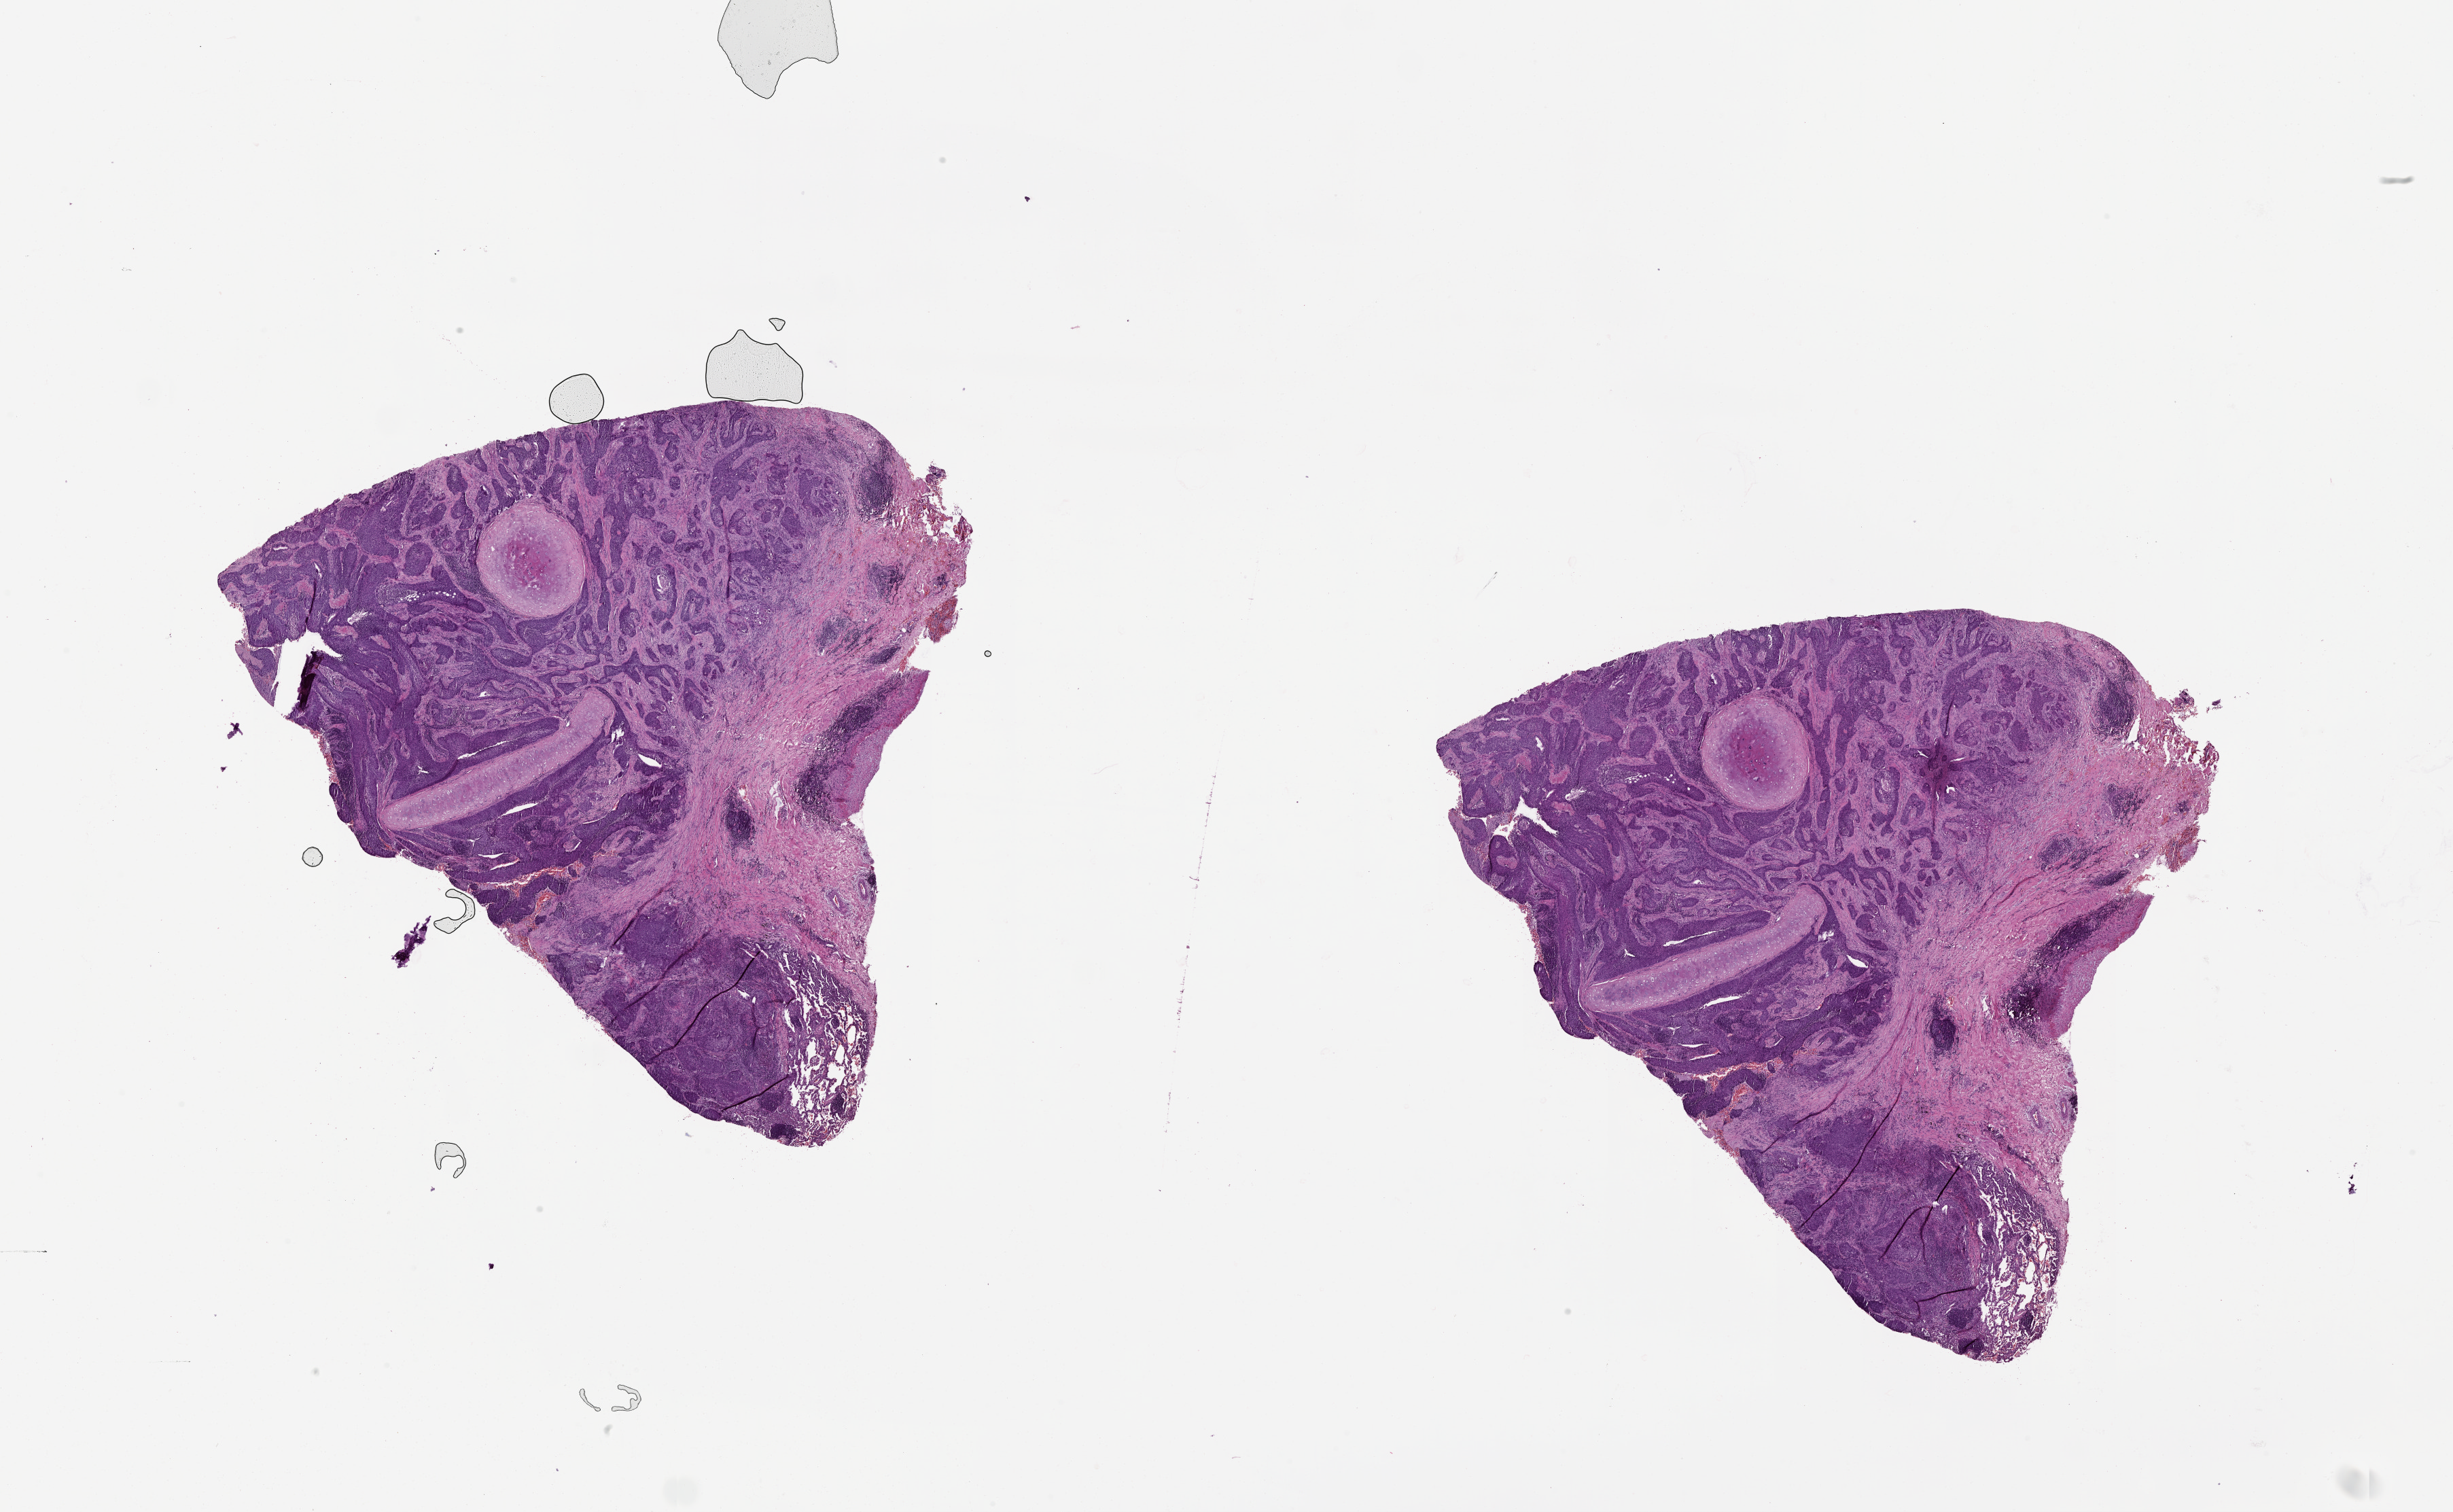
Hematoxylin and eosin (H&E) stained whole-slide image, whole scanned area (about 29.1 x 17.9 mm) shown as a low-resolution overview, lung, tumour tissue. Patient: male, age 53 years.
Patient diagnosis (cohort enrolment): squamous cell carcinoma (lung).